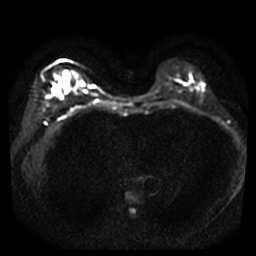
Breast MRI, one axial slice. Slice 16 of 40 in the series (ordered by position). Diffusion-weighted series; image 2 of 4 stored at this slice position (different b-values; order by instance number). 3 T. 5 mm slice thickness. 256 × 256 image matrix, field of view 320 × 320 mm. Female patient.
Annotated regions visible in this slice (expert manual segmentation):
- tumour on diffusion-weighted imaging: bounding box (x1, y1, x2, y2) in pixels: (61, 78, 66, 83)